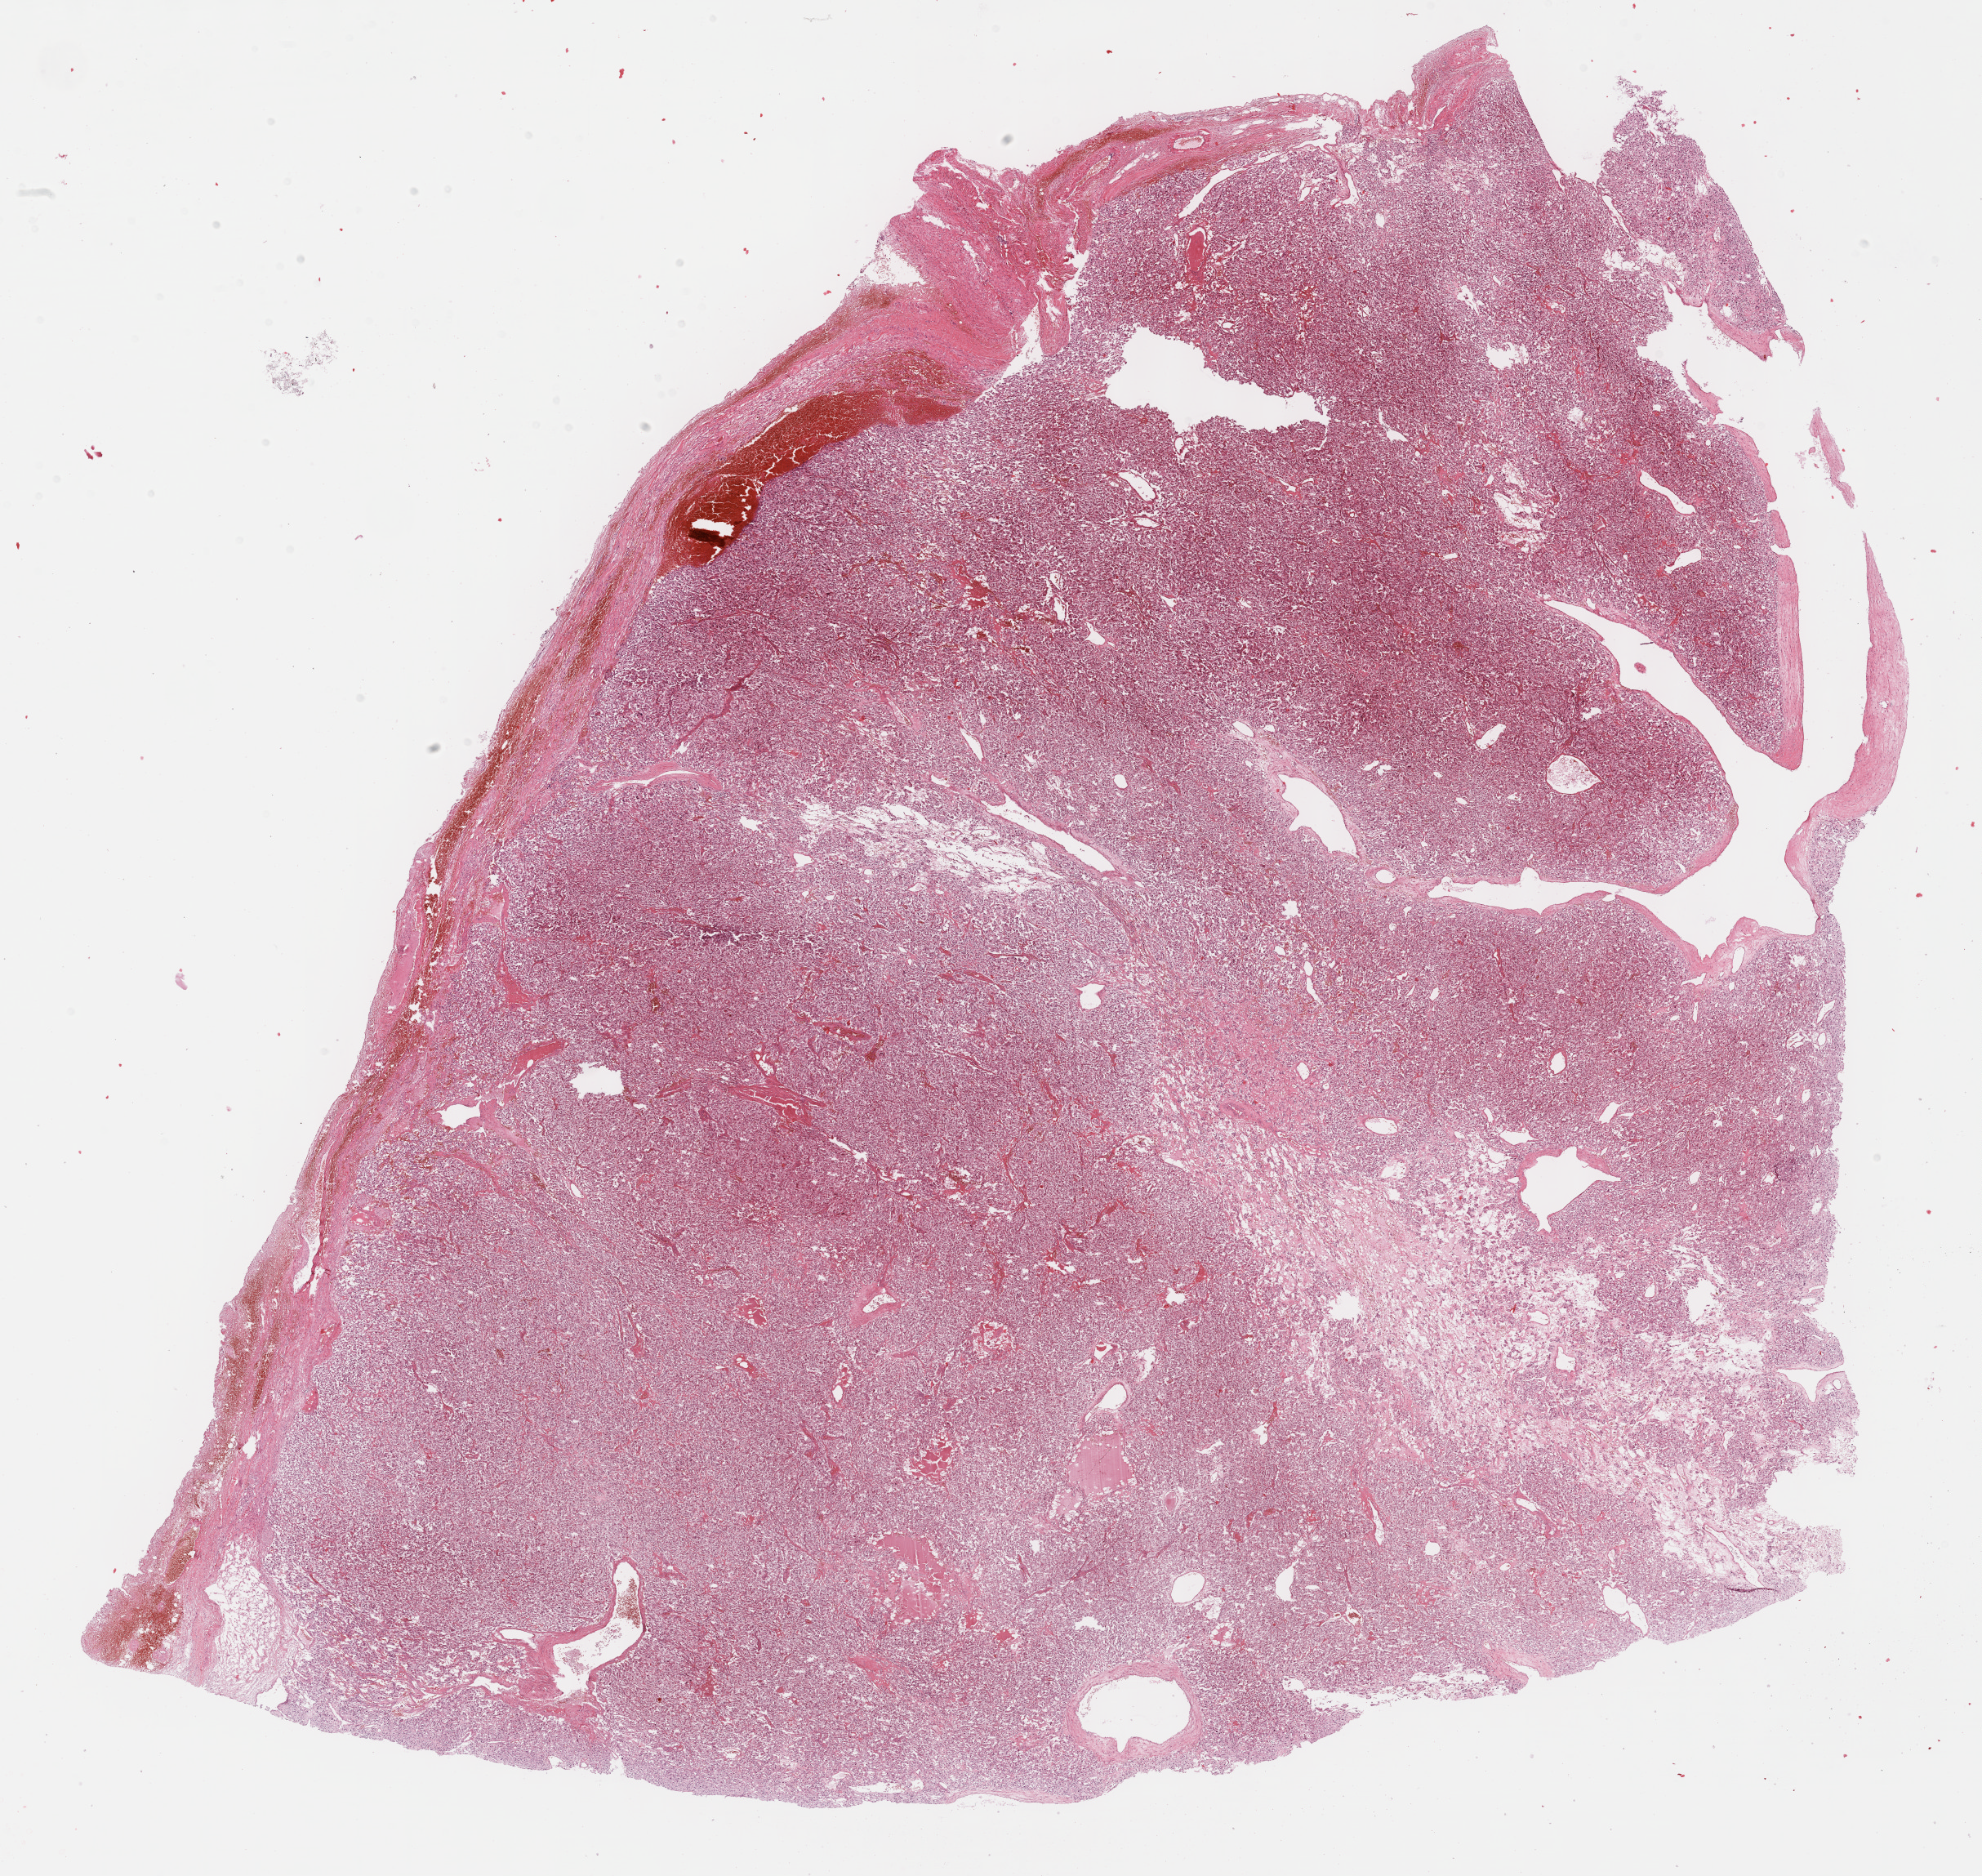
Digitized Hematoxylin and eosin (H&E) stained tissue section (whole slide), whole scanned area (about 19.6 x 18.6 mm) shown as a low-resolution overview. Formalin-fixed paraffin-embedded (FFPE) diagnostic section. Primary tumour sample from the connective, subcutaneous and other soft tissues. Female, age 75 years at initial diagnosis.
- pathologic diagnosis: Extra-adrenal paraganglioma, NOS (connective, subcutaneous and other soft tissues of pelvis)